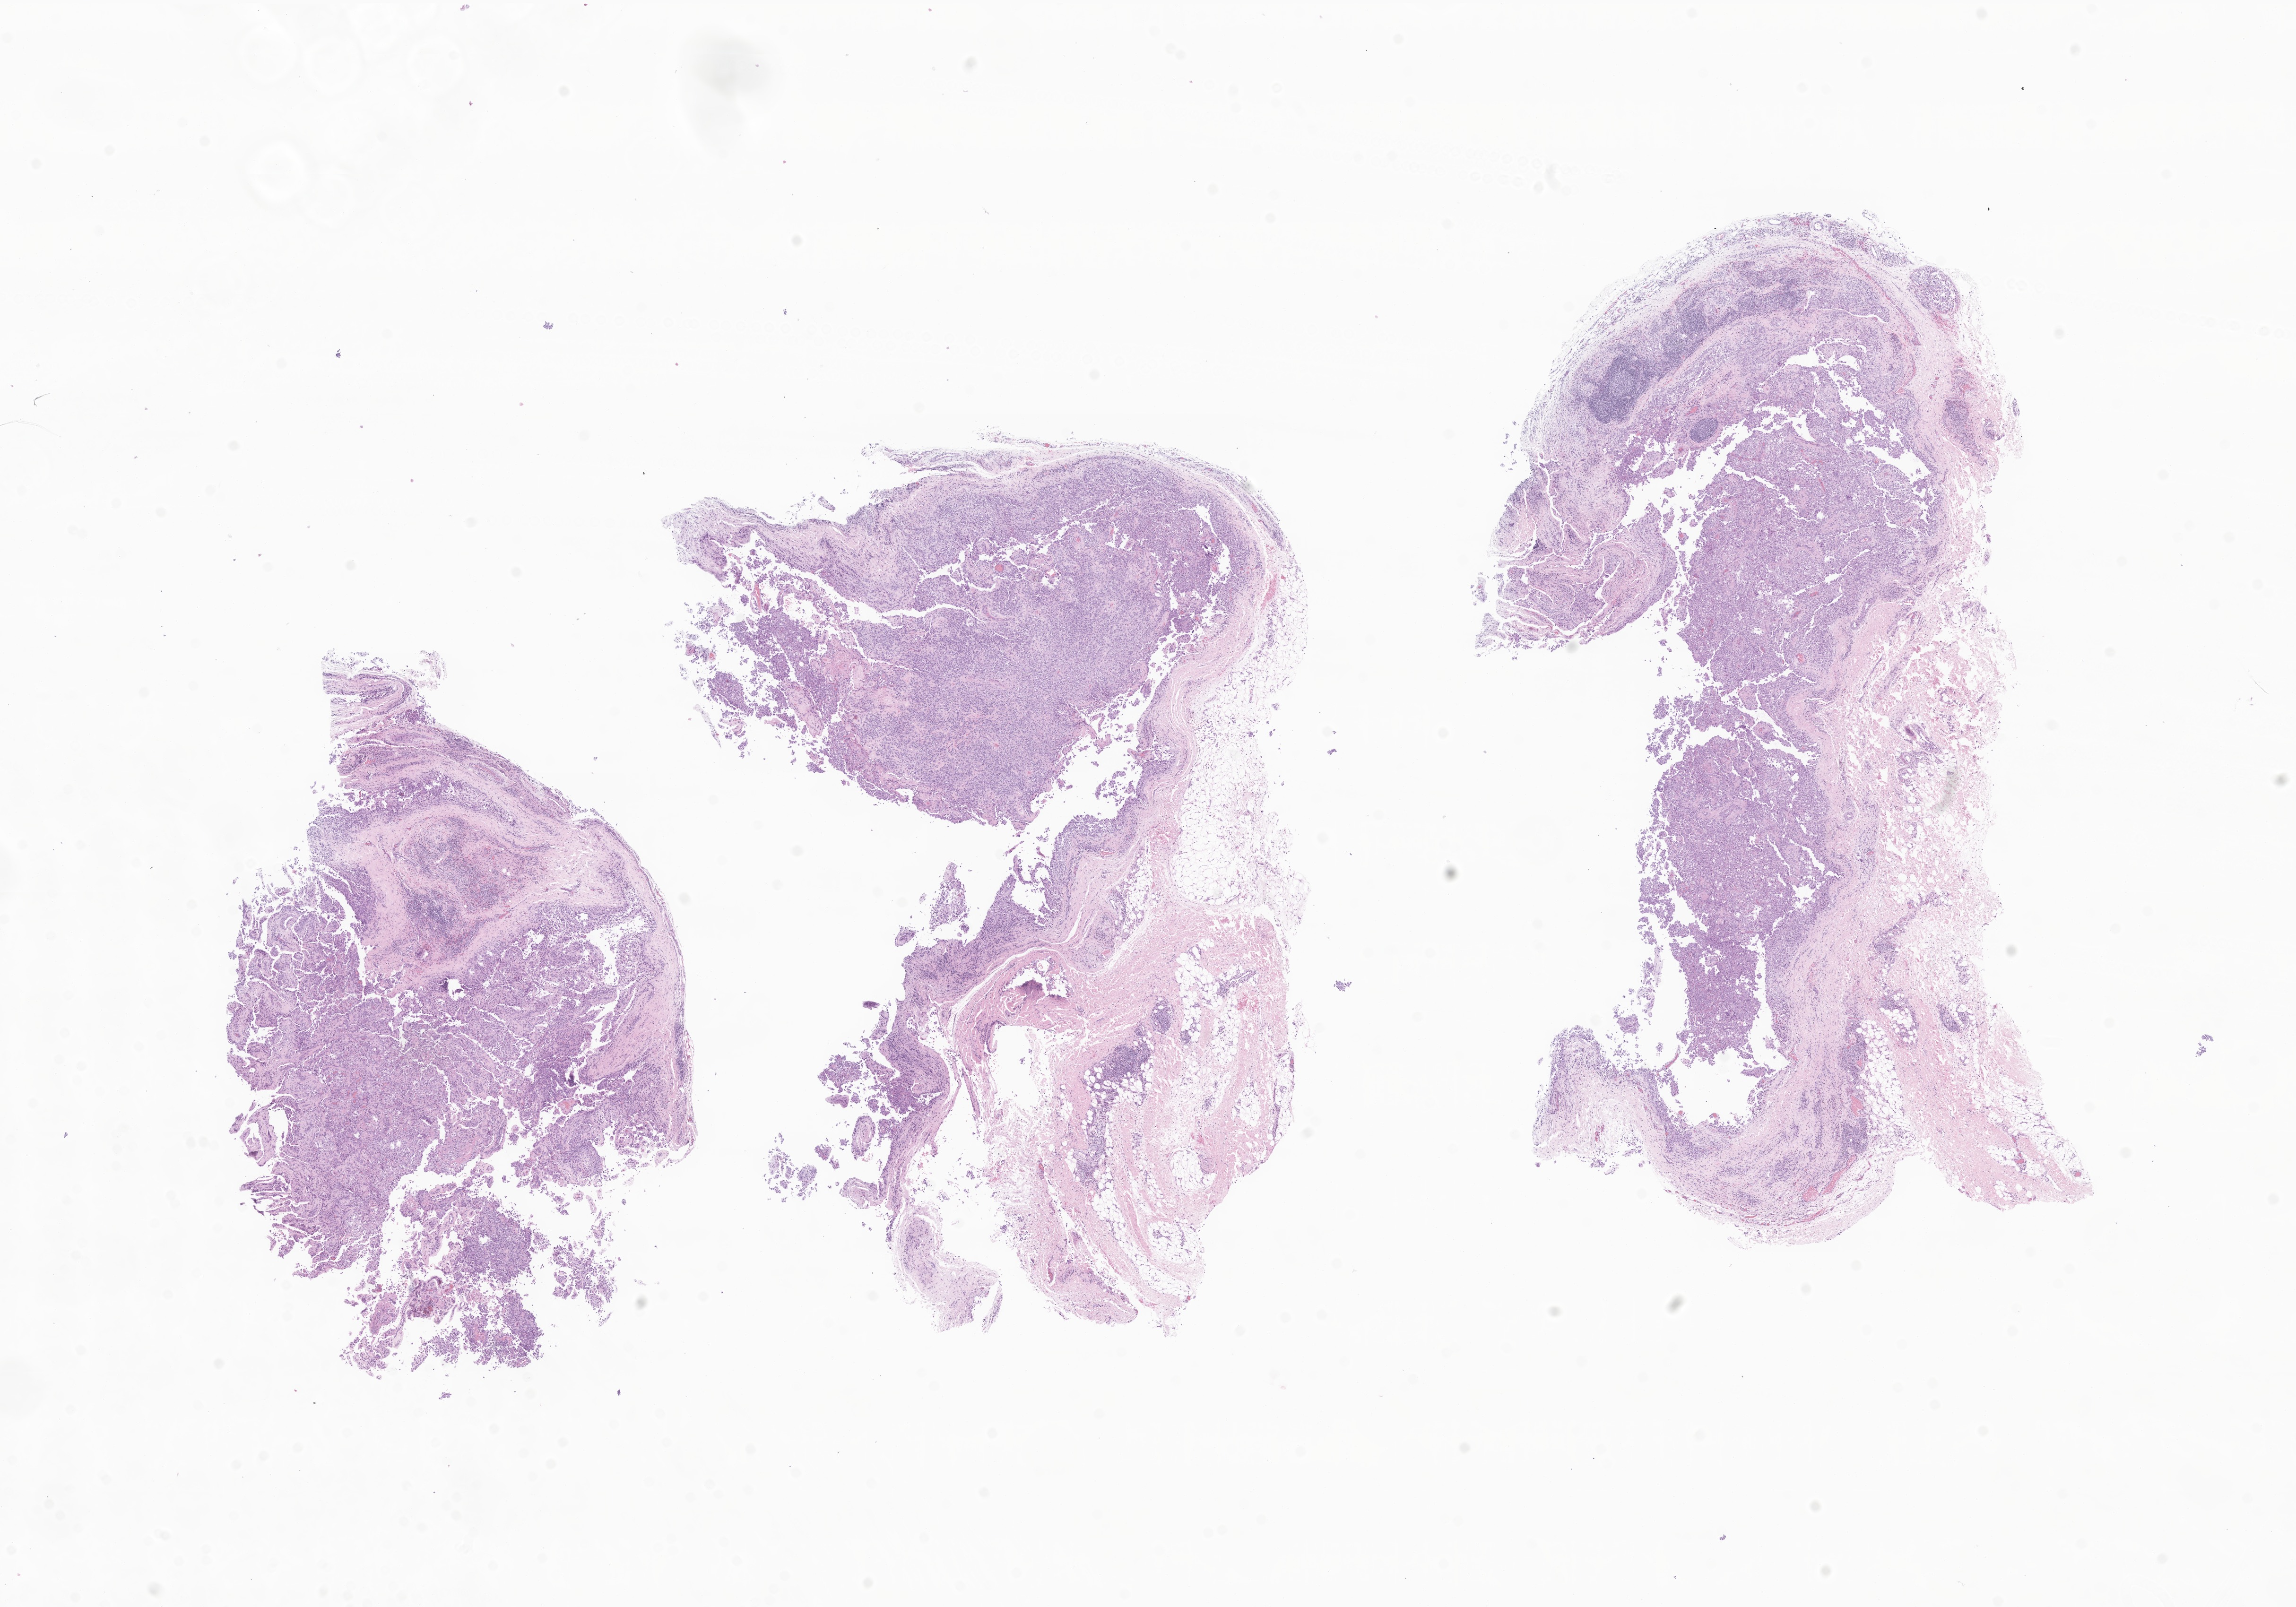
Whole-slide image, haematoxylin and eosin stain of tumor tissue from the upper limb — whole scanned area (about 20.5 x 14.3 mm) shown as a low-resolution overview, formalin-fixed paraffin-embedded section. Patient: male, age 38 months.
Diagnosis (ICD-O-3 morphology term): Epithelial-myoepithelial carcinoma.